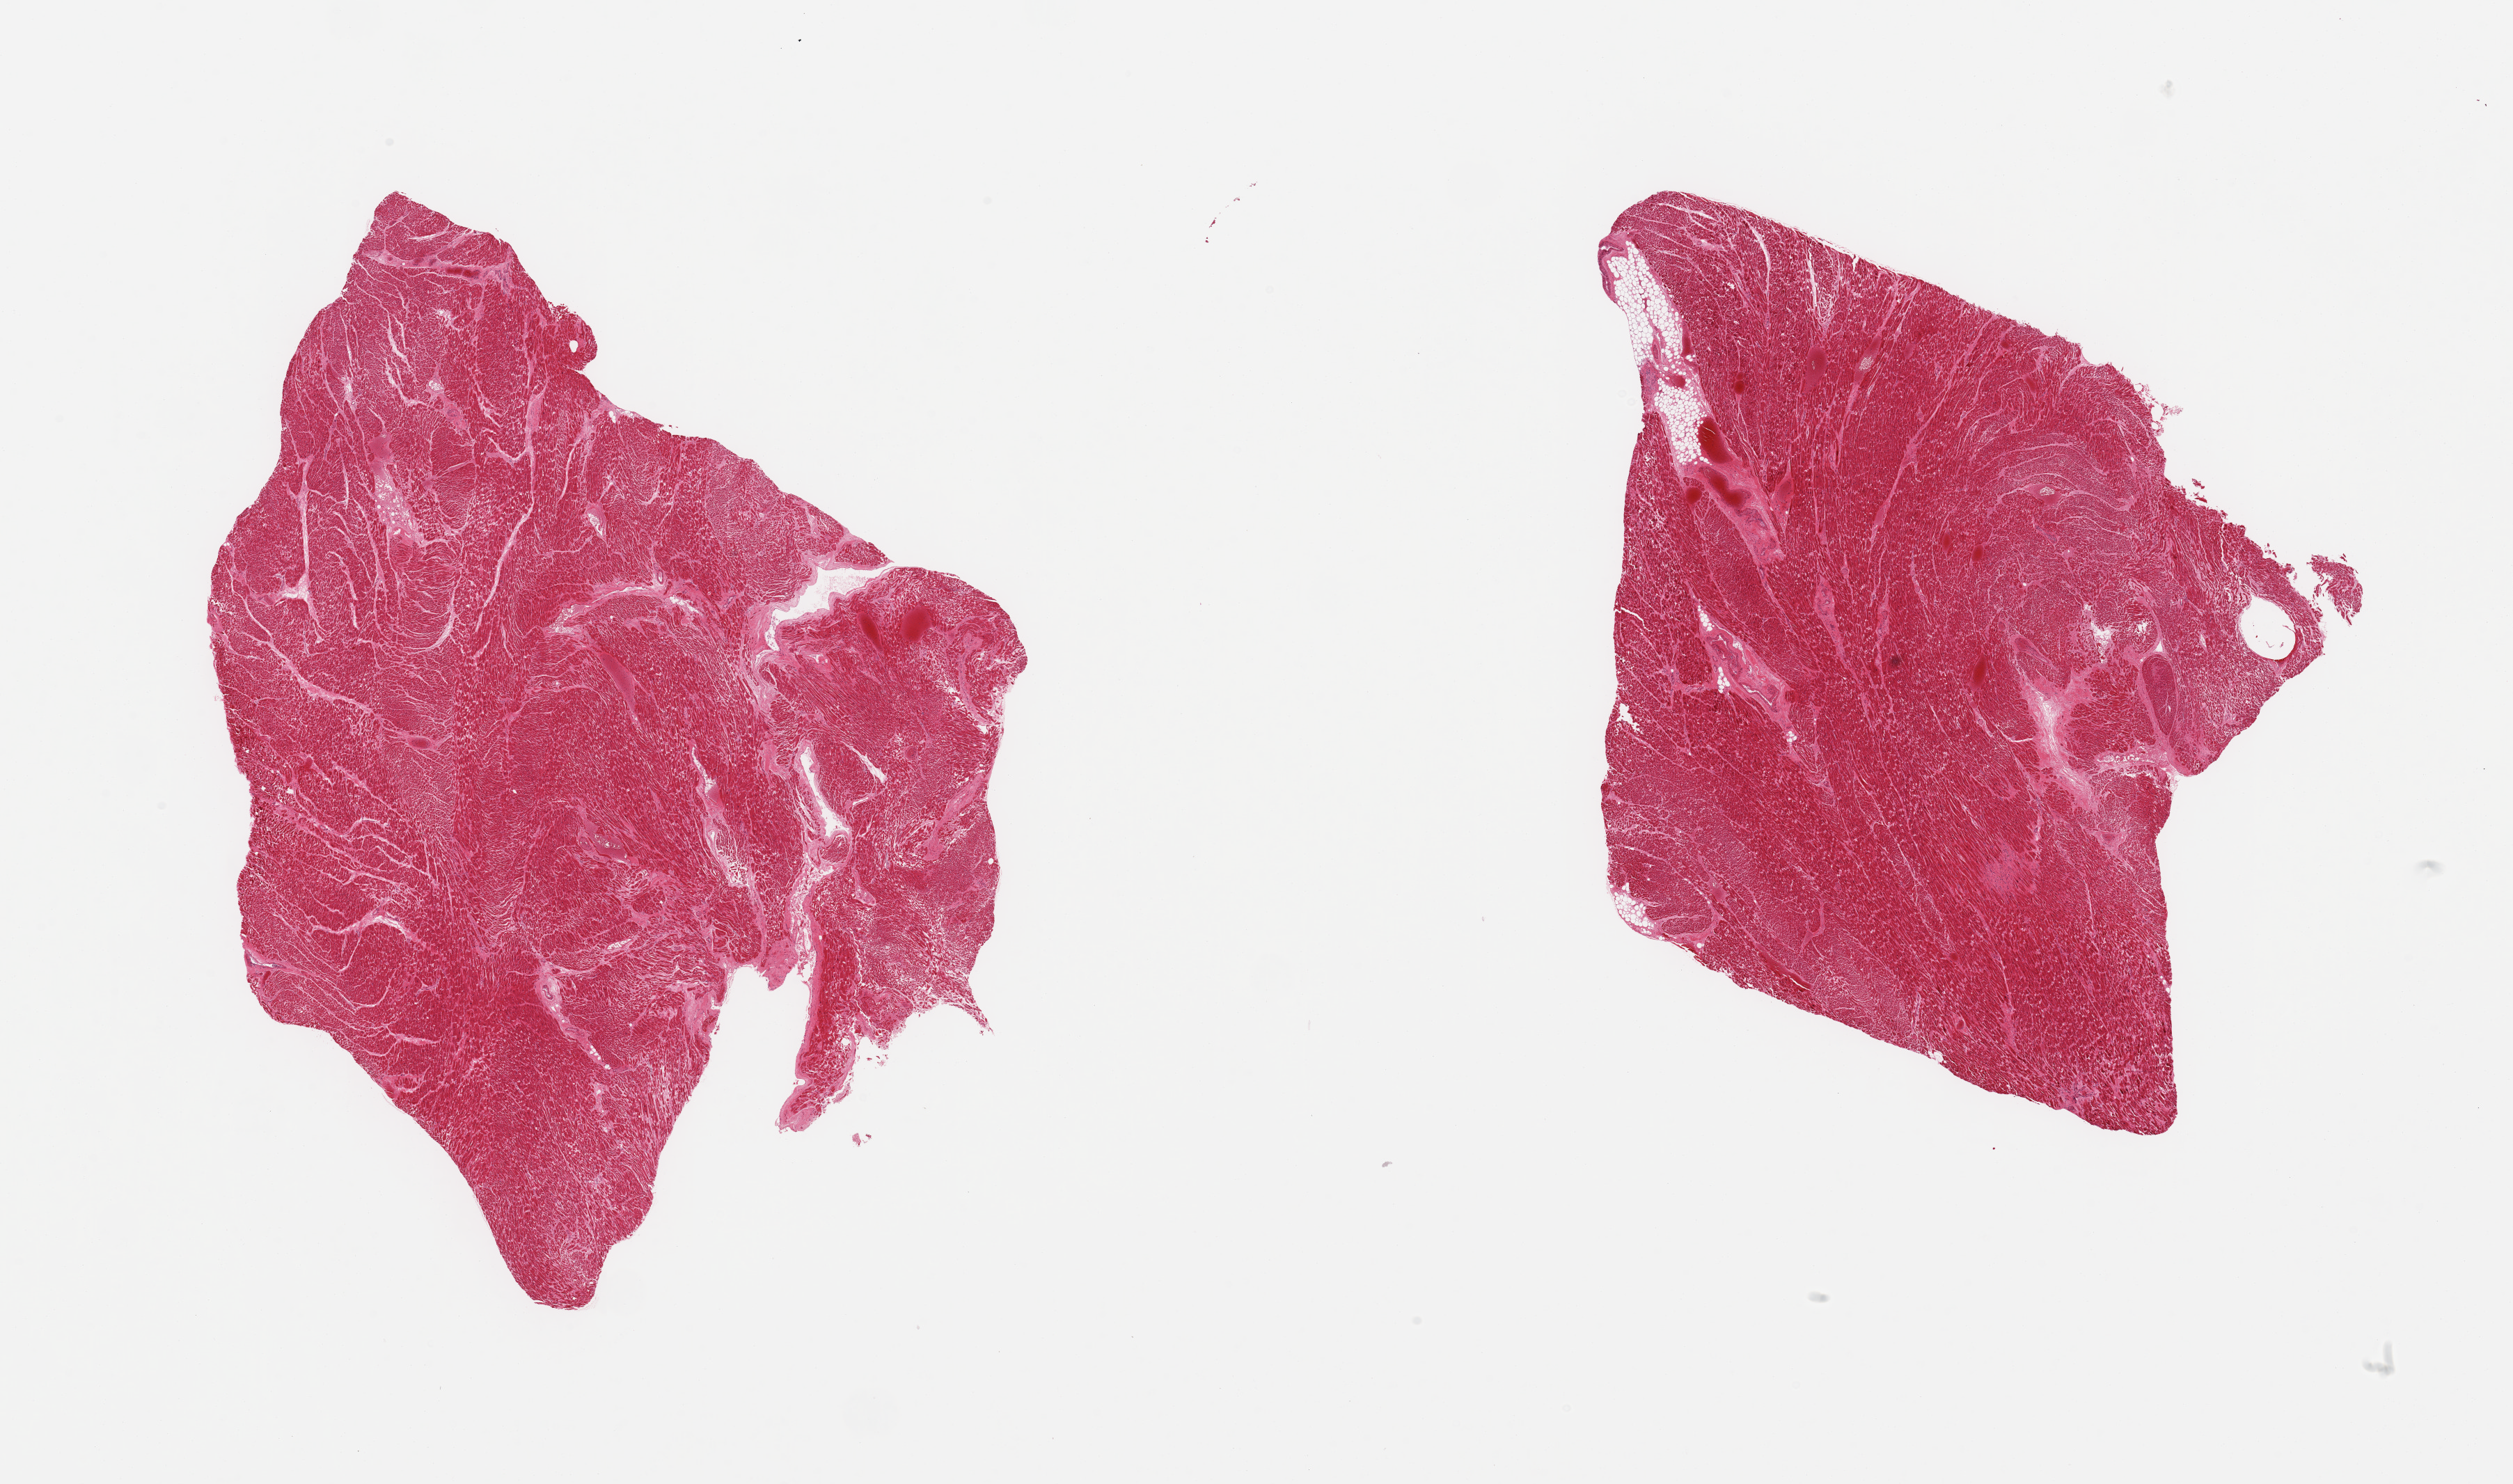
Whole-slide image, H&E stain, brightfield, shown as a low-resolution overview of the whole scanned area (about 28.5 x 16.9 mm). PAXgene-fixed, paraffin-embedded tissue. Target tissue: heart. Donor tissue sample. Donor: male.
• pathologist's review note for this sample: 2 pieces; patchy eosinophilia and few foci of scar, trivial component of fat